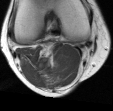
MRI of an extremity soft-tissue mass, one axial slice. Position 11 of 45 along the scan axis. MR volume resampled by the dataset authors to the PET/CT grid (not the native acquisition matrix). 3.27 mm slice thickness. 113 × 111 image matrix, field of view 110 × 108 mm. Female patient. From the clinical record (not read from this slice): histological type: liposarcoma; site of the primary tumour: right thigh.
Structures marked on this image (expert contour drawn on MRI and transferred to this co-registered scan by the dataset authors):
- gross tumour volume (mass): bounding box <42,65,63,84> (left, top, right, bottom; pixels)